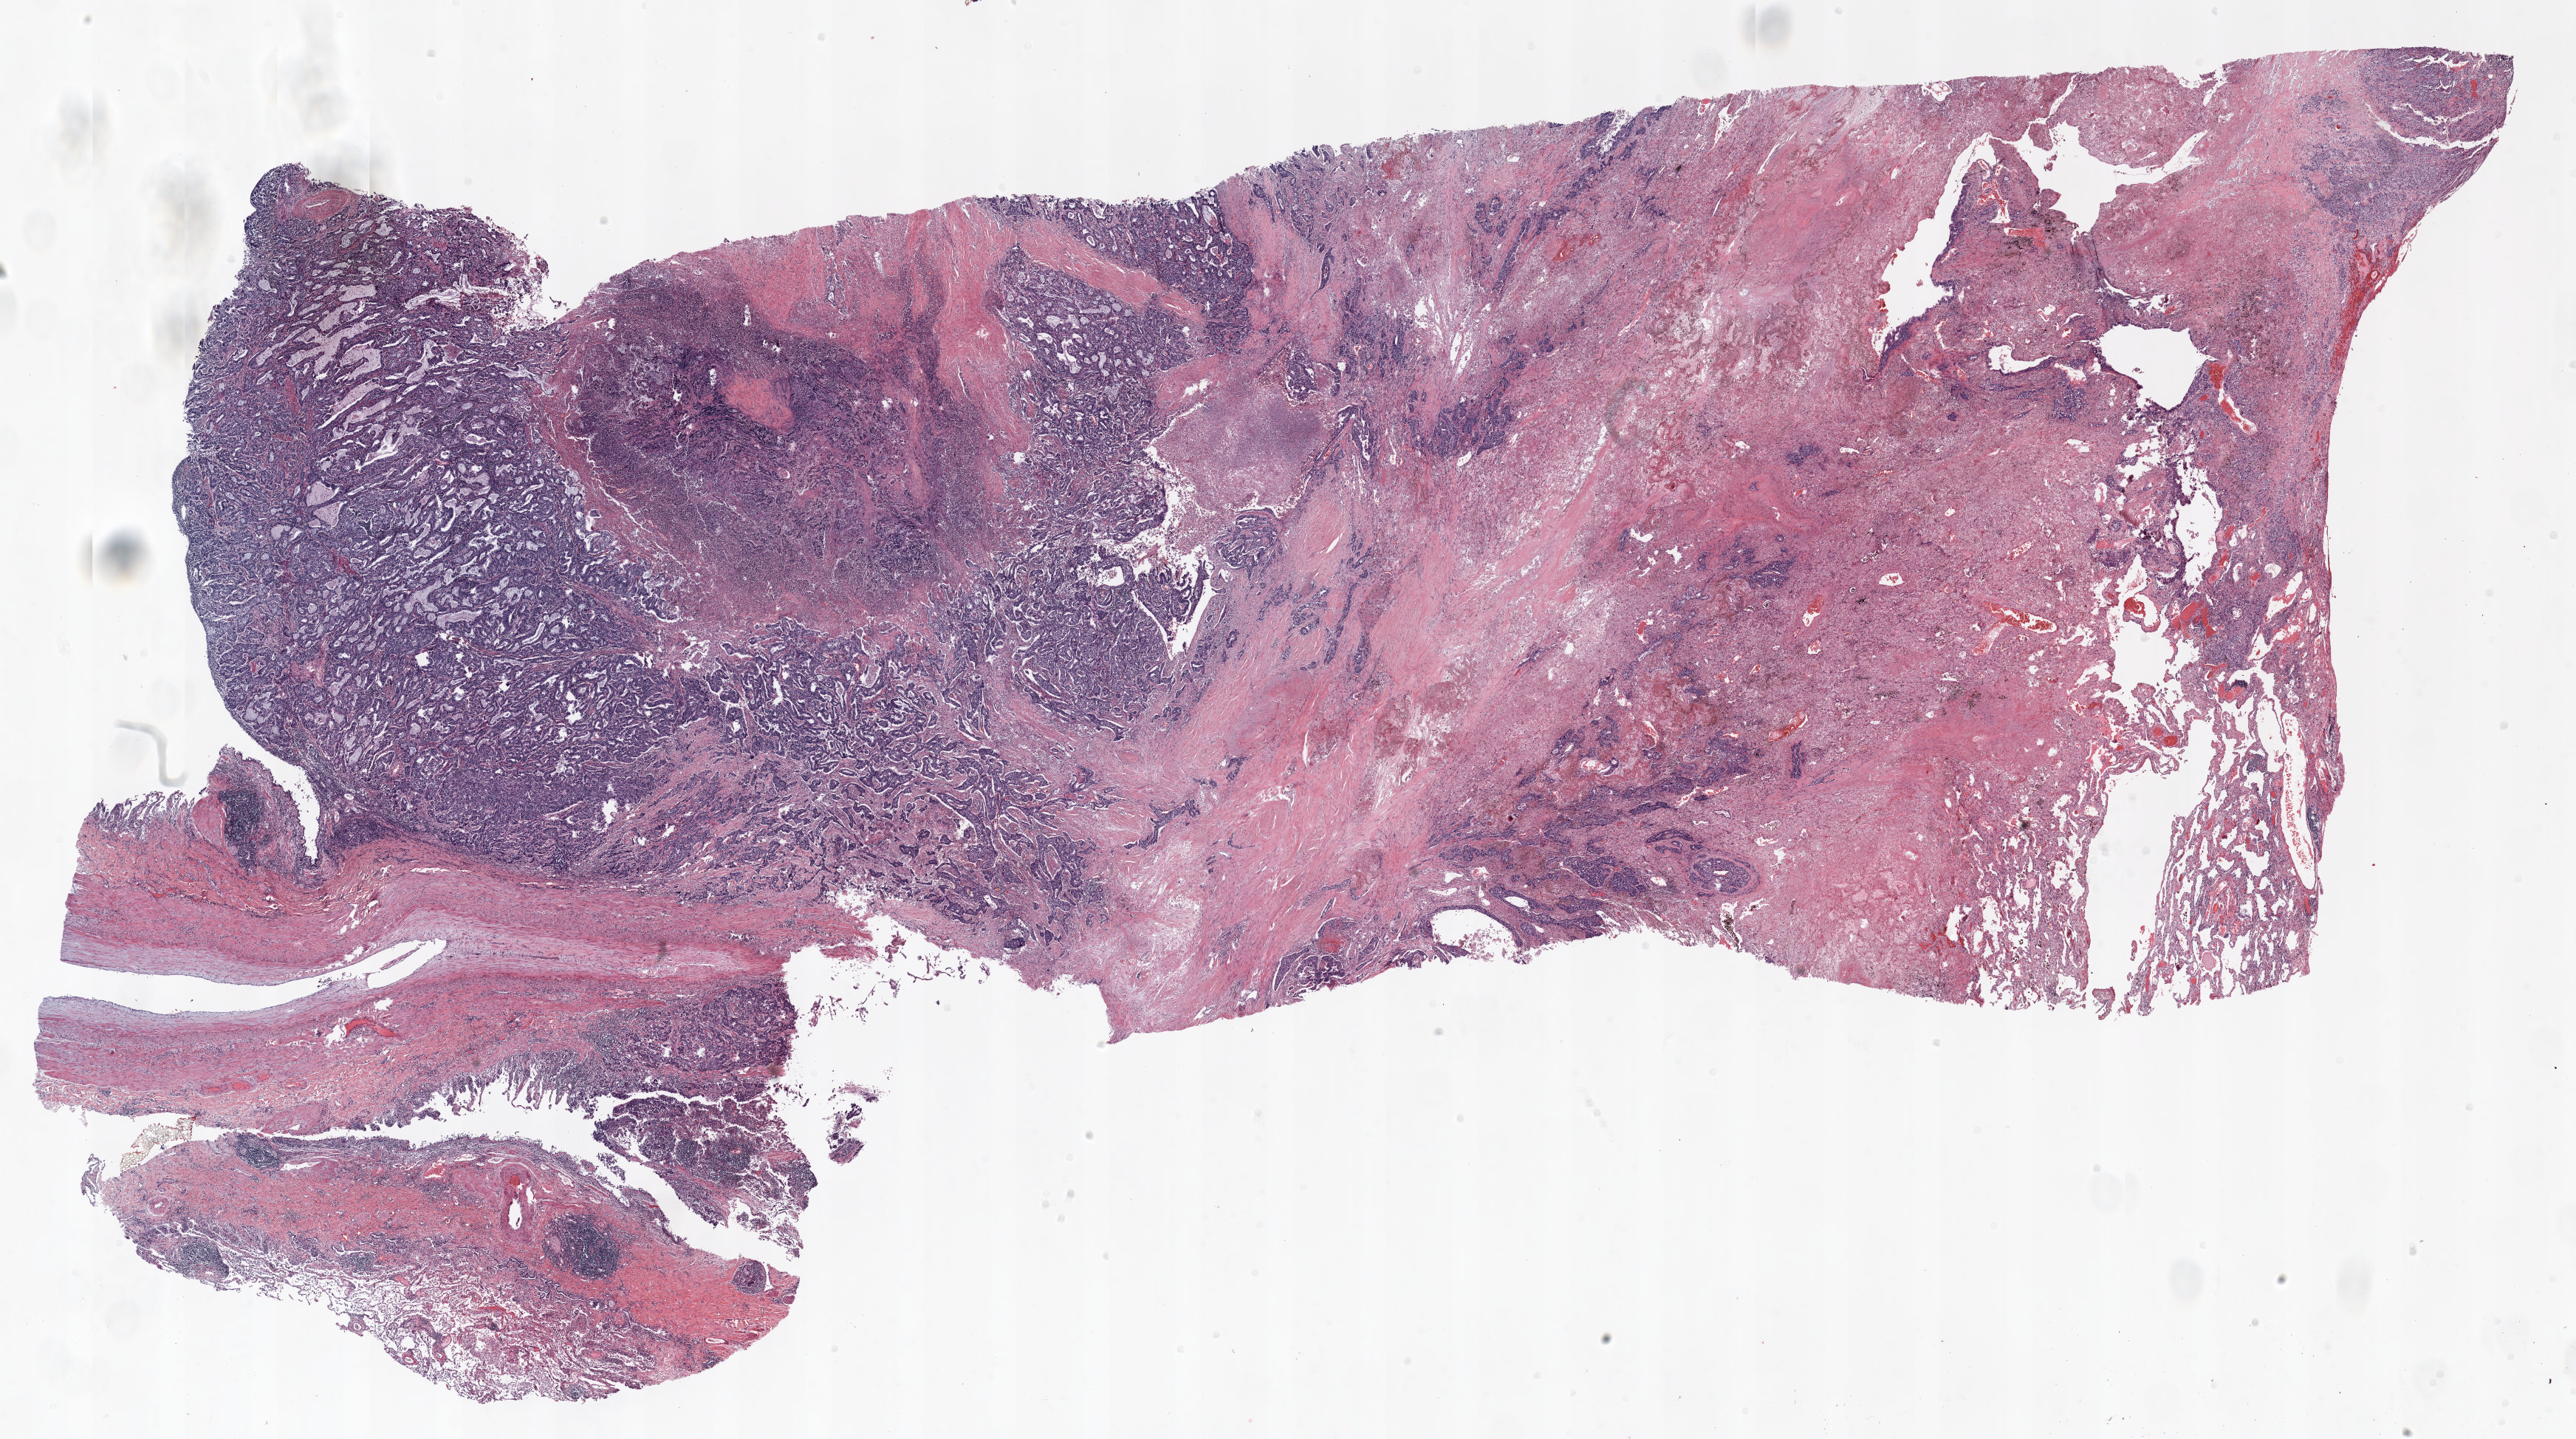
Whole-slide histology image, Hematoxylin and eosin (H&E) stained — whole scanned area (about 28.0 x 15.7 mm) shown as a low-resolution overview; FFPE section; lung. Male patient, aged 64 at enrolment. Current smoker at enrolment. Grade: moderately differentiated (G2).
Primary tumour location (clinical record): left upper lobe. Stage (AJCC 6th edition): IA. Tumour size (pathology): 29 mm. Participant's lung-cancer diagnosis: Adenocarcinoma, NOS.